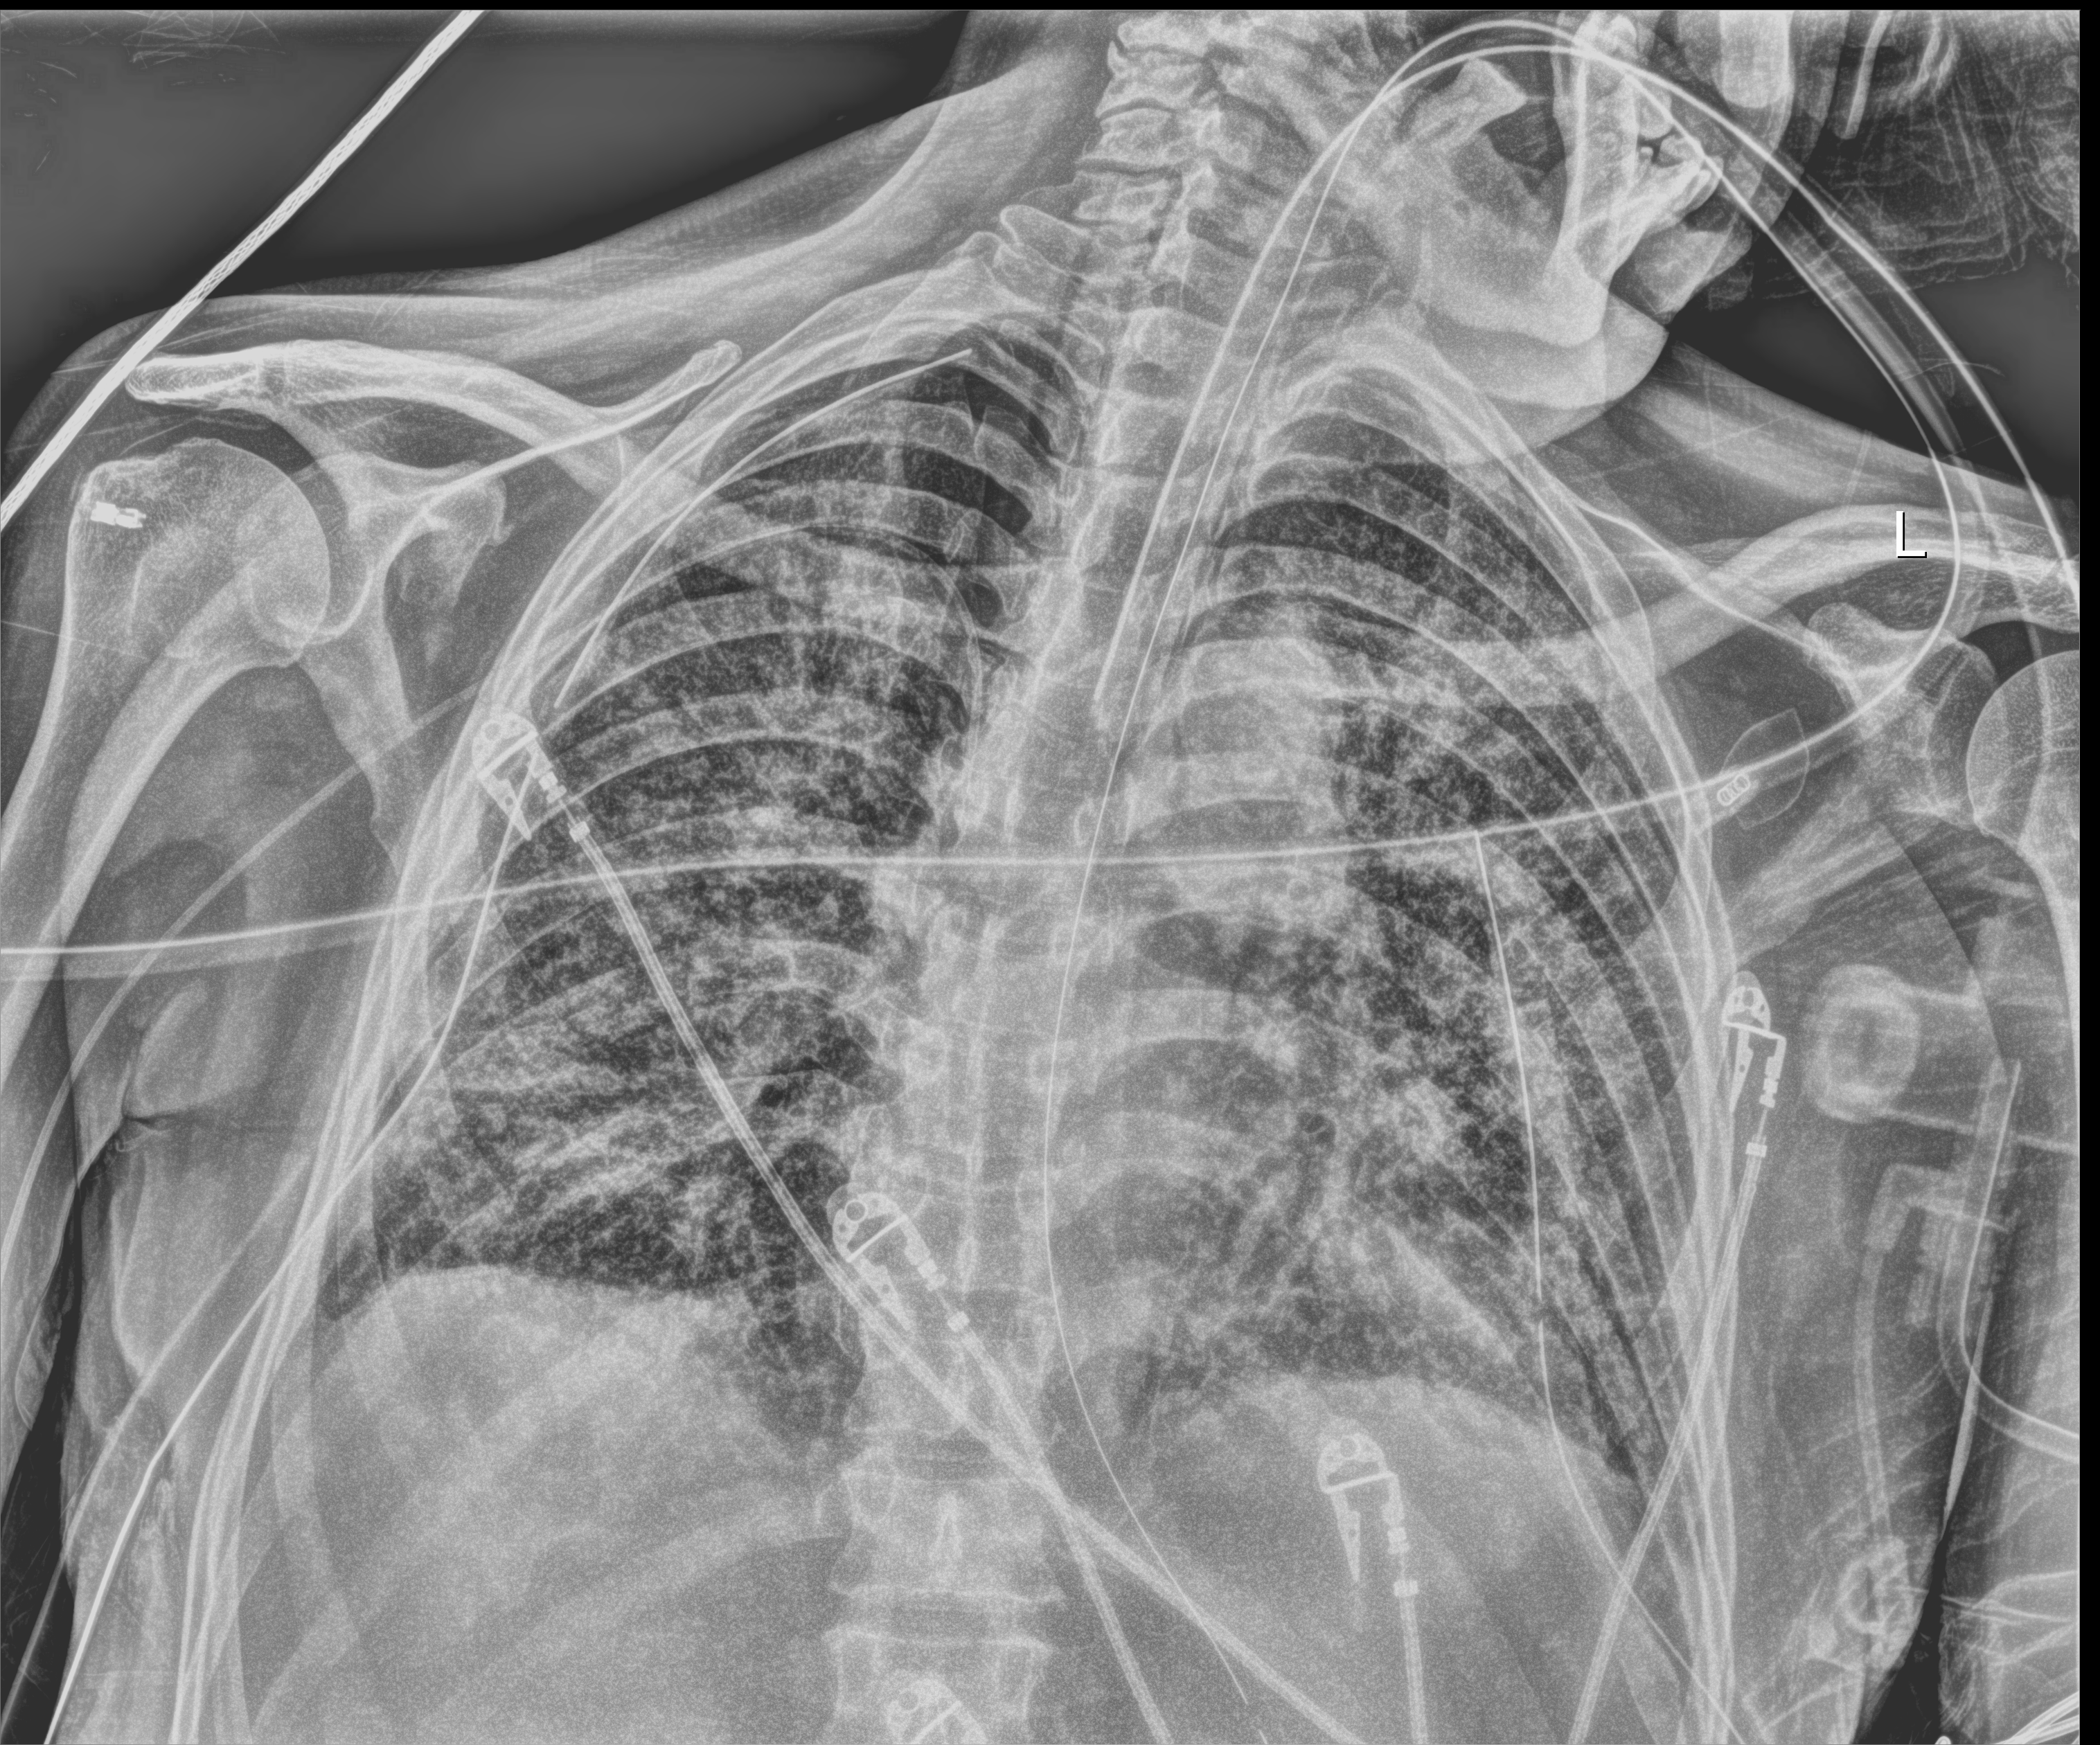
Chest radiograph, anteroposterior (AP) projection. Male patient hospitalised with COVID-19, age 60–74 years.
Hospital-stay facts (about this admission, not read from this image; timing relative to this image not recorded):
- admitted to intensive care during this hospital stay: yes
- length of hospital stay: 65 days
- mechanically ventilated during this hospital stay: yes